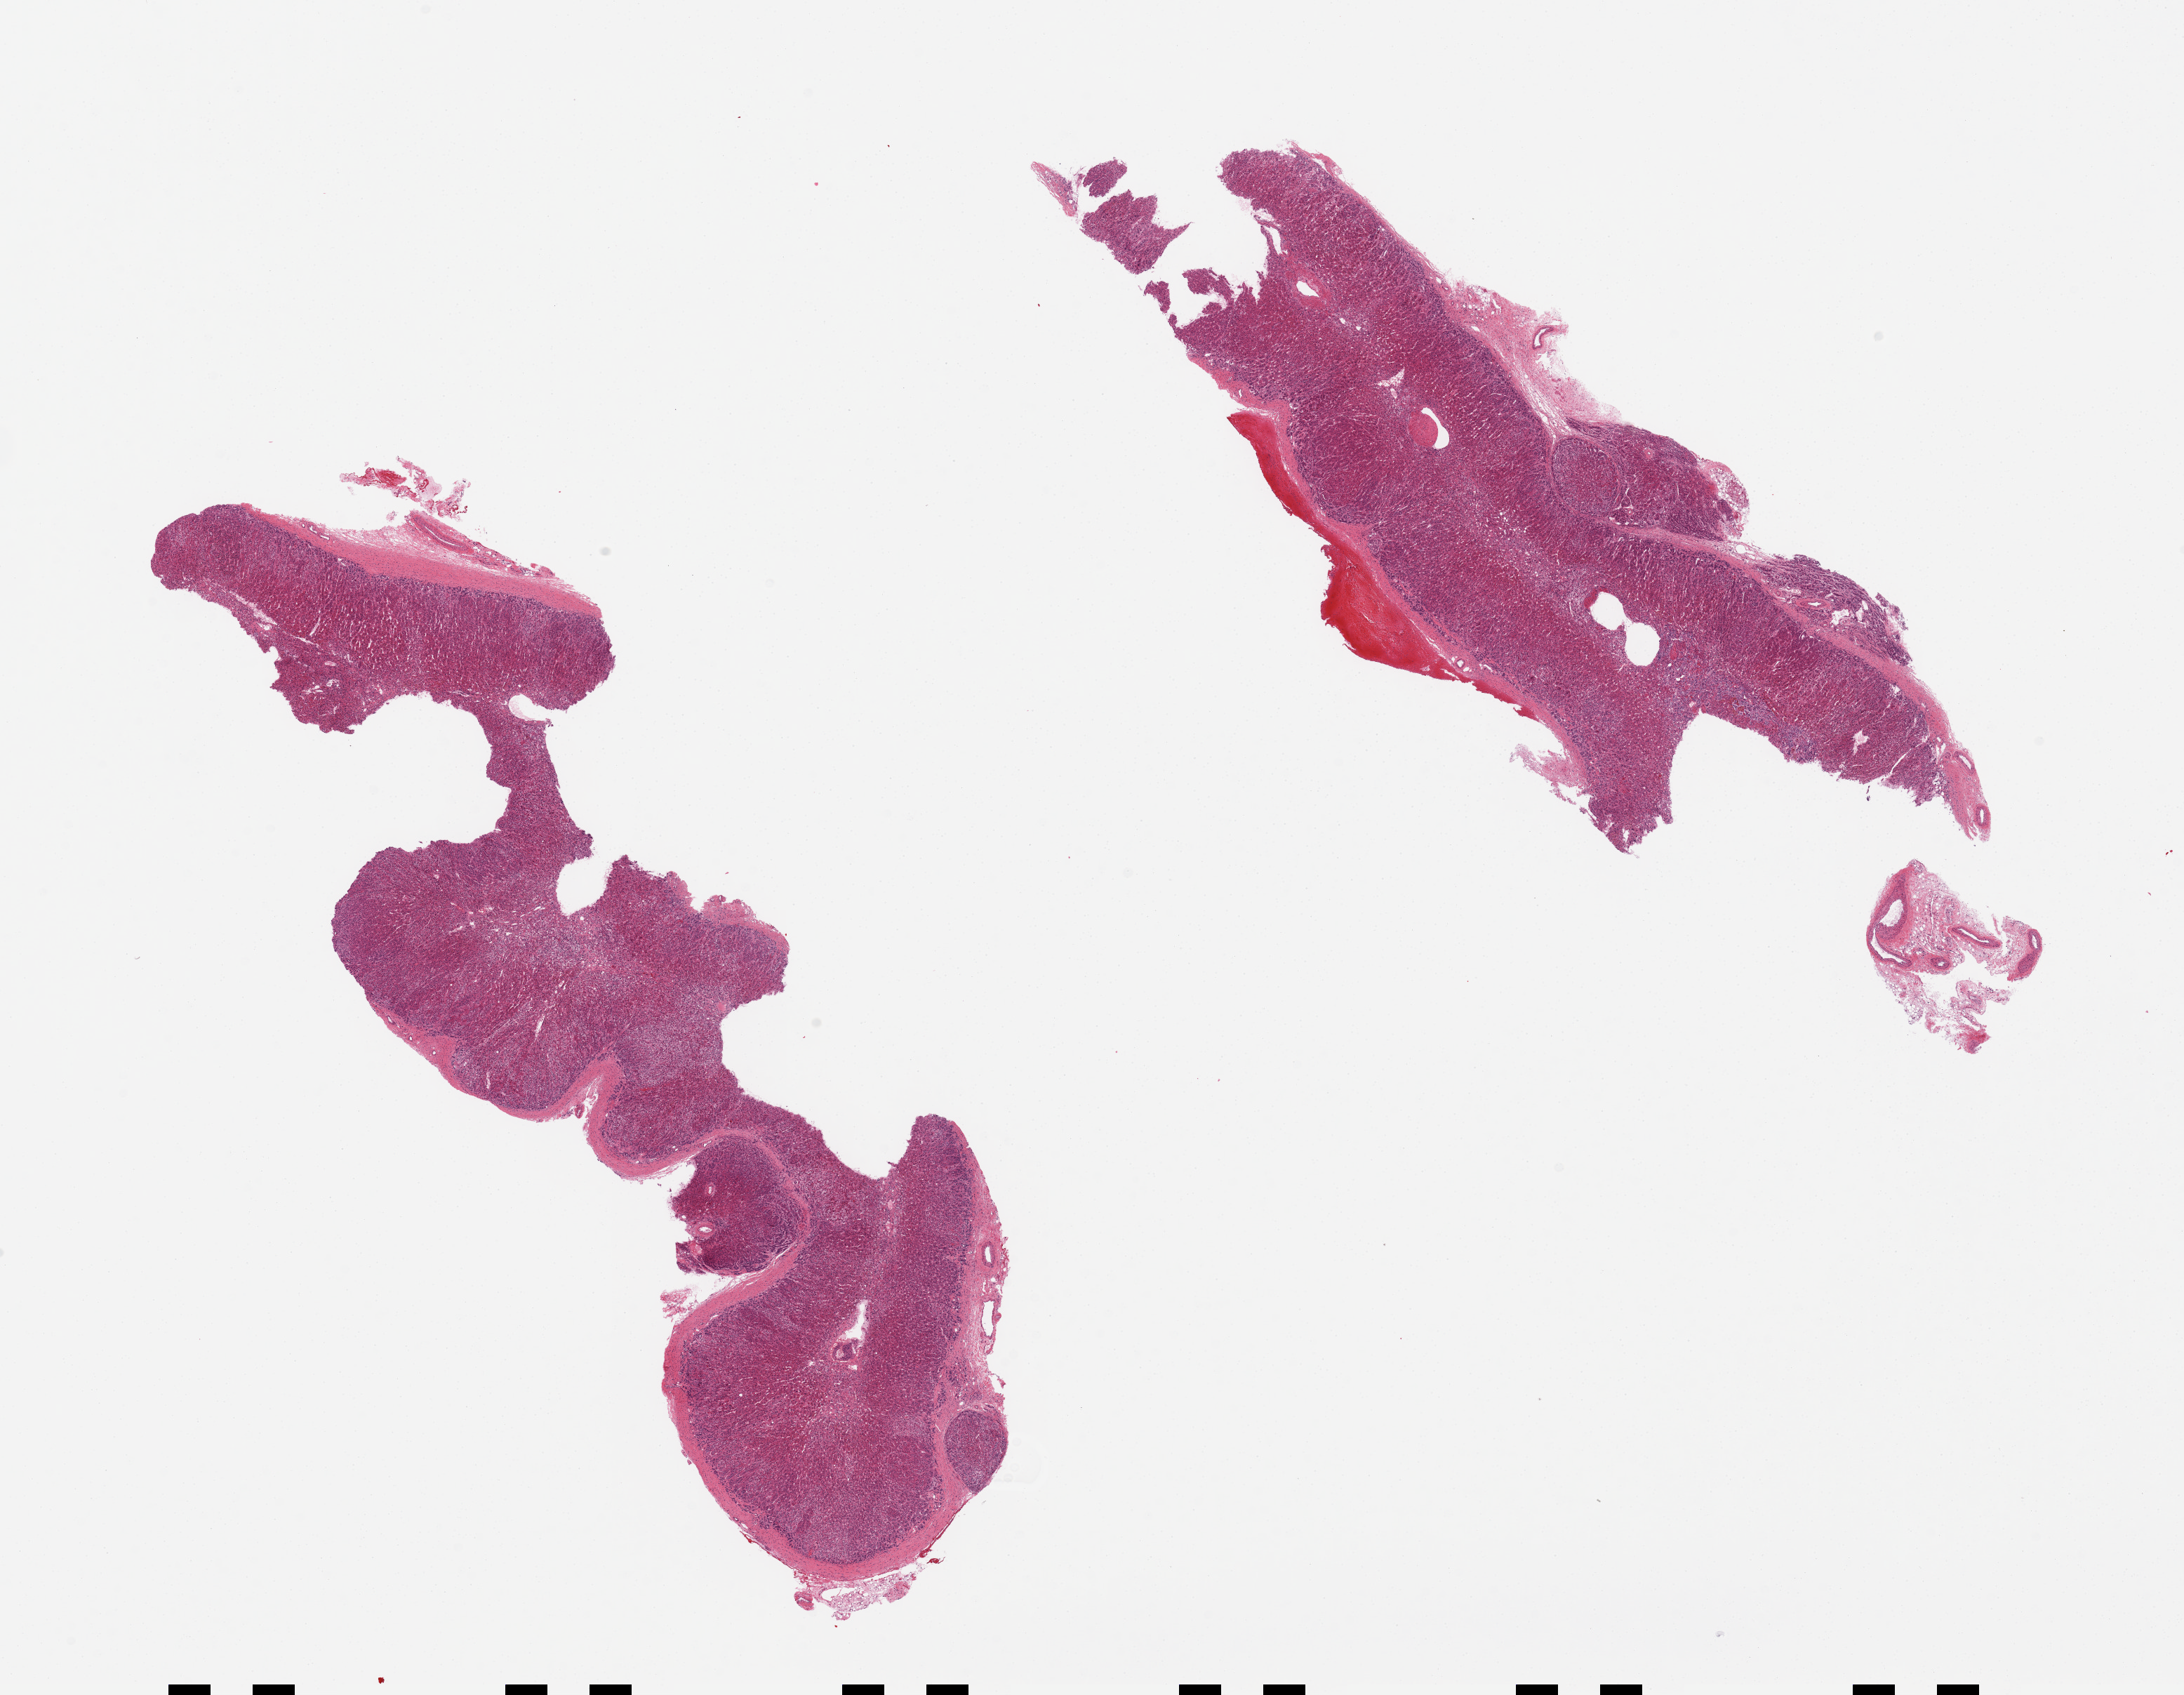
H&E whole-slide image, a low-resolution overview of the entire scanned area, about 24.6 x 19.1 mm; PAXgene-fixed paraffin-embedded (PFPE) section; sampled site (target tissue): adrenal gland; donor tissue sample. Donor sex: male.
Pathologist's review note for this sample: 2 pieces; well dissected, no fat, focal periadrenal hemorrhage.